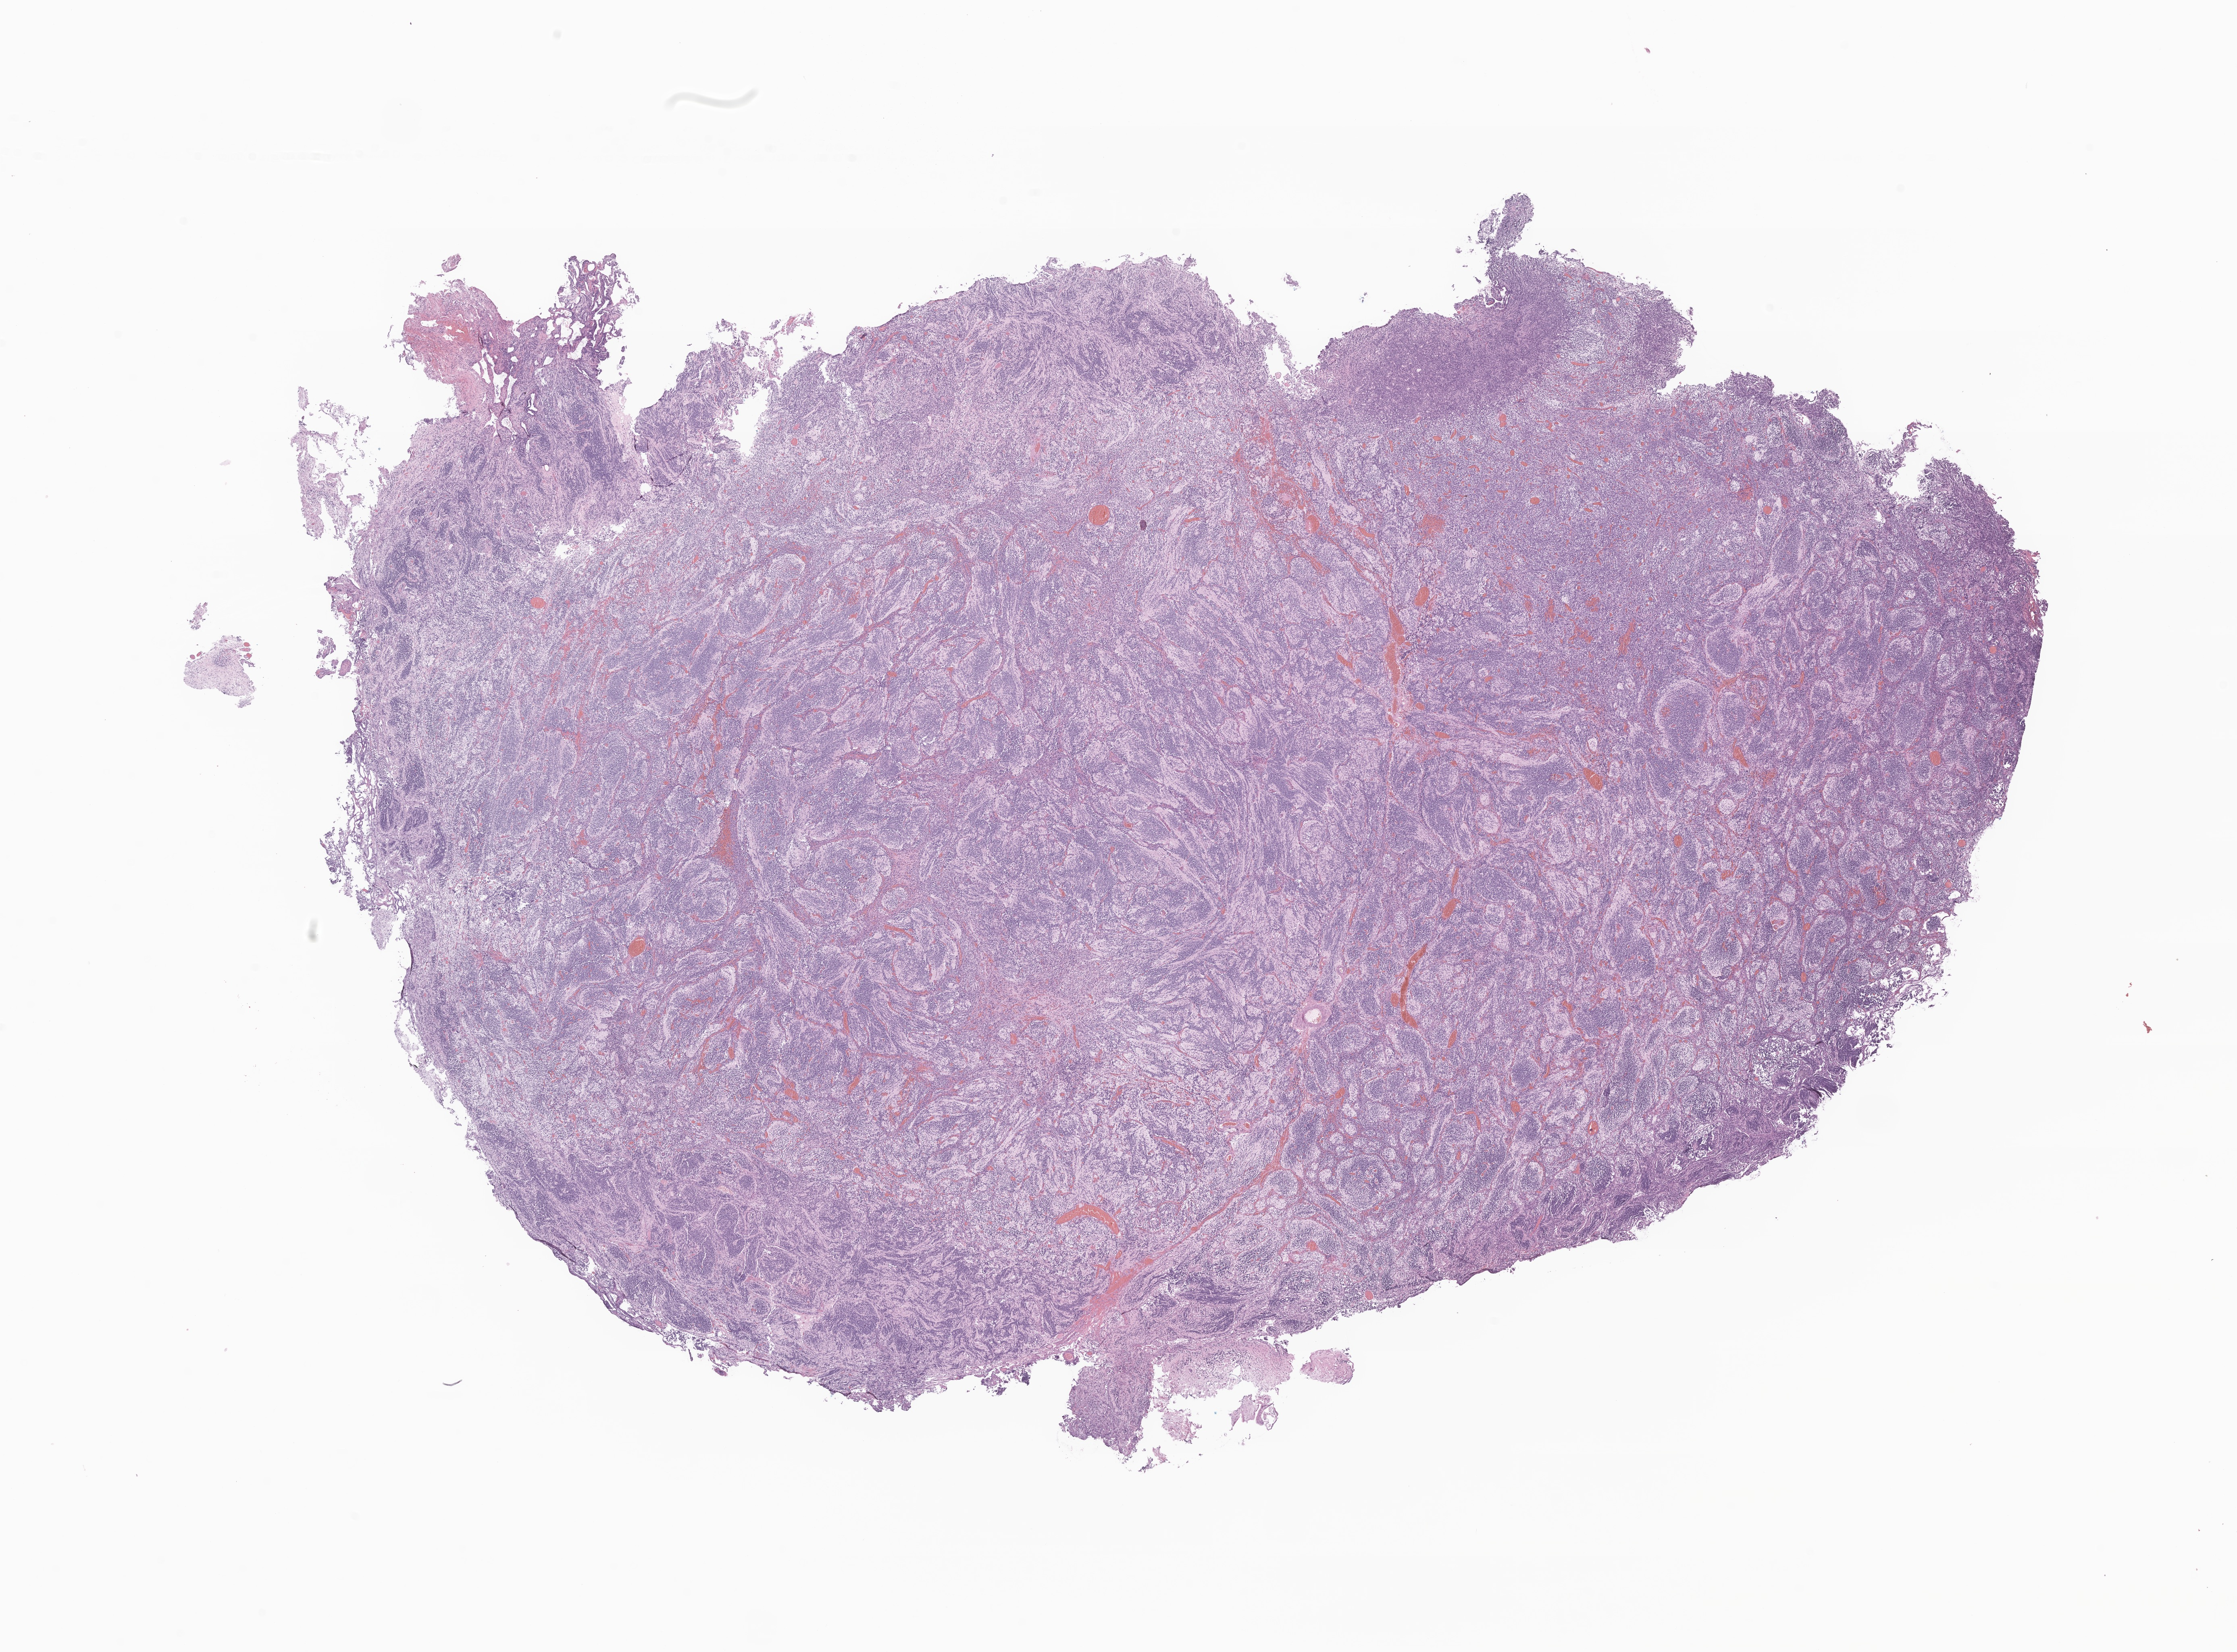
Digitized haematoxylin and eosin-stained section of tumor tissue from the cerebellum — a low-resolution overview of the entire scanned area, about 23.4 x 17.3 mm. FFPE section. Patient: female, age 213 days.
* diagnosis (ICD-O-3 morphology term): Medulloblastoma, NOS